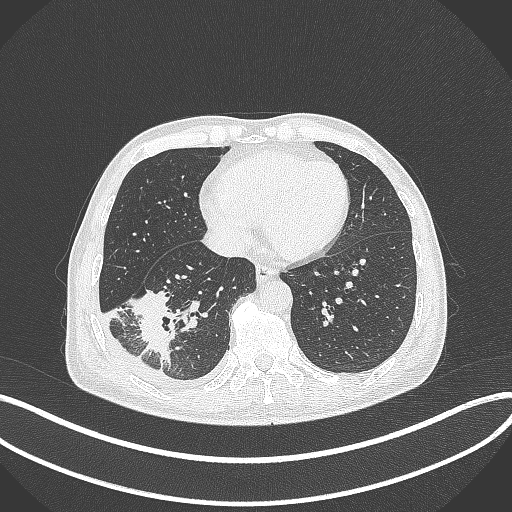
Chest CT, one axial slice. Position 124 of 388 along the scan axis. Reconstruction kernel B70f. 120 kVp. Lung window (W 1500 / L -600 HU). 1 mm slice thickness. 512 × 512 image matrix, field of view 400 × 400 mm. Male patient, age 64 years. From the clinical record (not read from this slice): clinical TNM (as recorded): T3 N0 M0; histopathological grade: G2-3.
Outlined on this slice (bounding box drawn by a radiologist):
- lung tumour (recorded histology: adenocarcinoma): box from (x=124, y=287) to (x=175, y=363) px